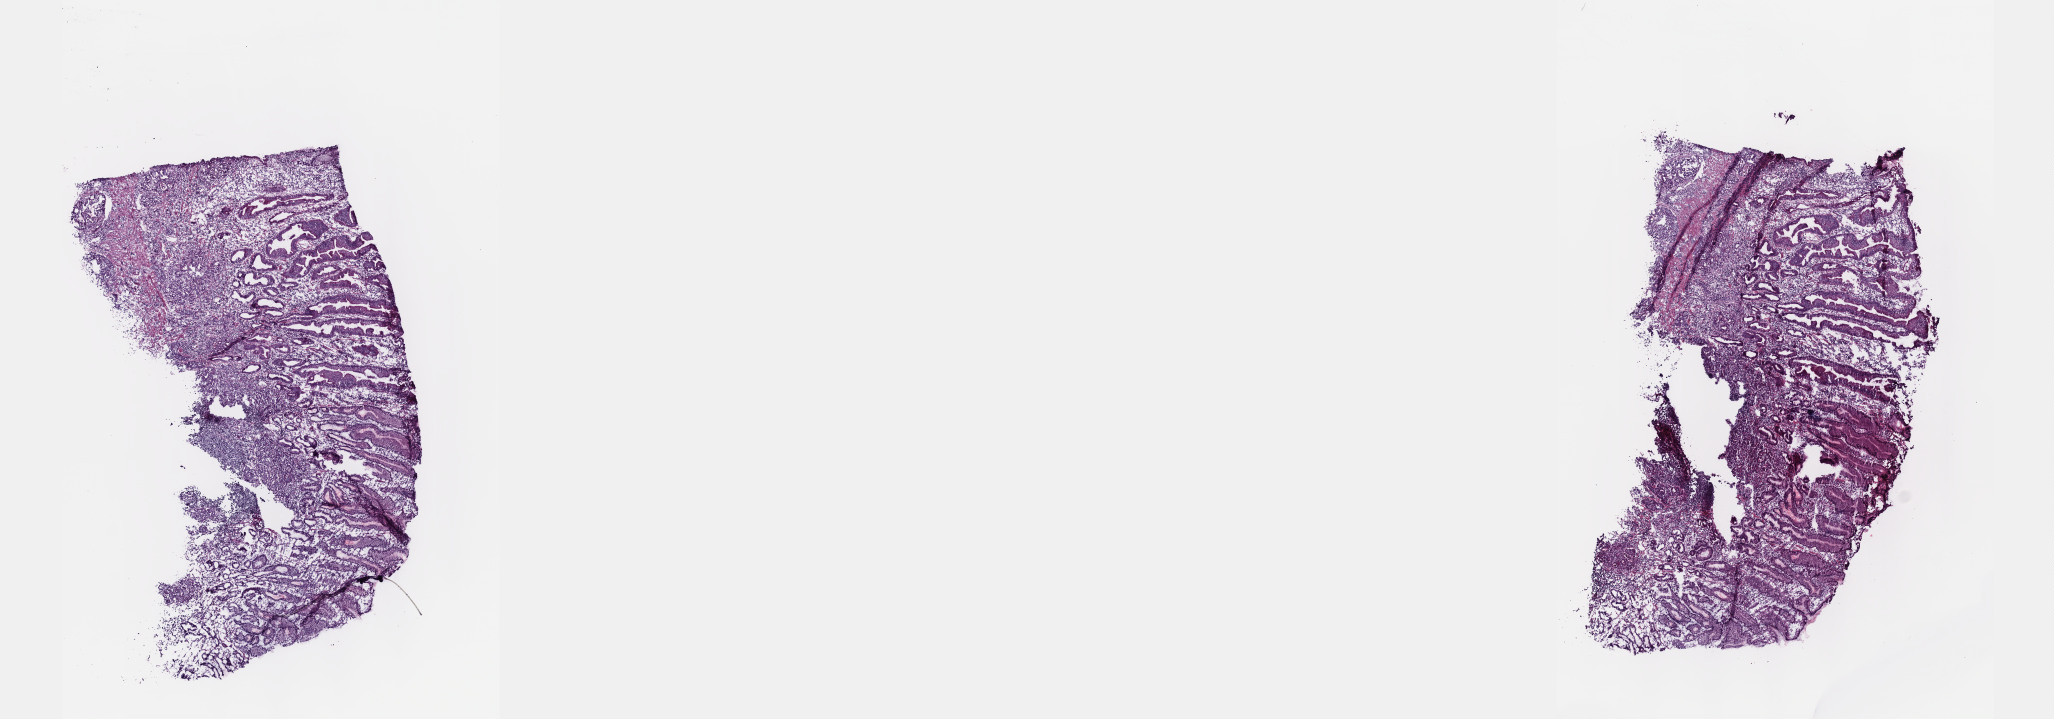
H&E whole-slide image — whole scanned area (about 16.6 x 5.8 mm, slide scanned at 40x) shown as a low-resolution overview; frozen section; stomach, primary tumour sample. Patient: male, age at initial diagnosis 76 years. Histologic grade: G2 (moderately differentiated). Composition of this section per pathologist review: tumour cells 60%, tumour nuclei 60%, normal cells 7%, stromal cells 33%, necrosis 0%. Inflammatory infiltration, as recorded: lymphocyte infiltration 5%, monocyte infiltration 2%, neutrophil infiltration 3%.
• AJCC pathologic stage: IV (6th edition)
• pathologic diagnosis: Tubular adenocarcinoma (body of stomach)
• lymph nodes positive (case pathology): 3 of 19 examined